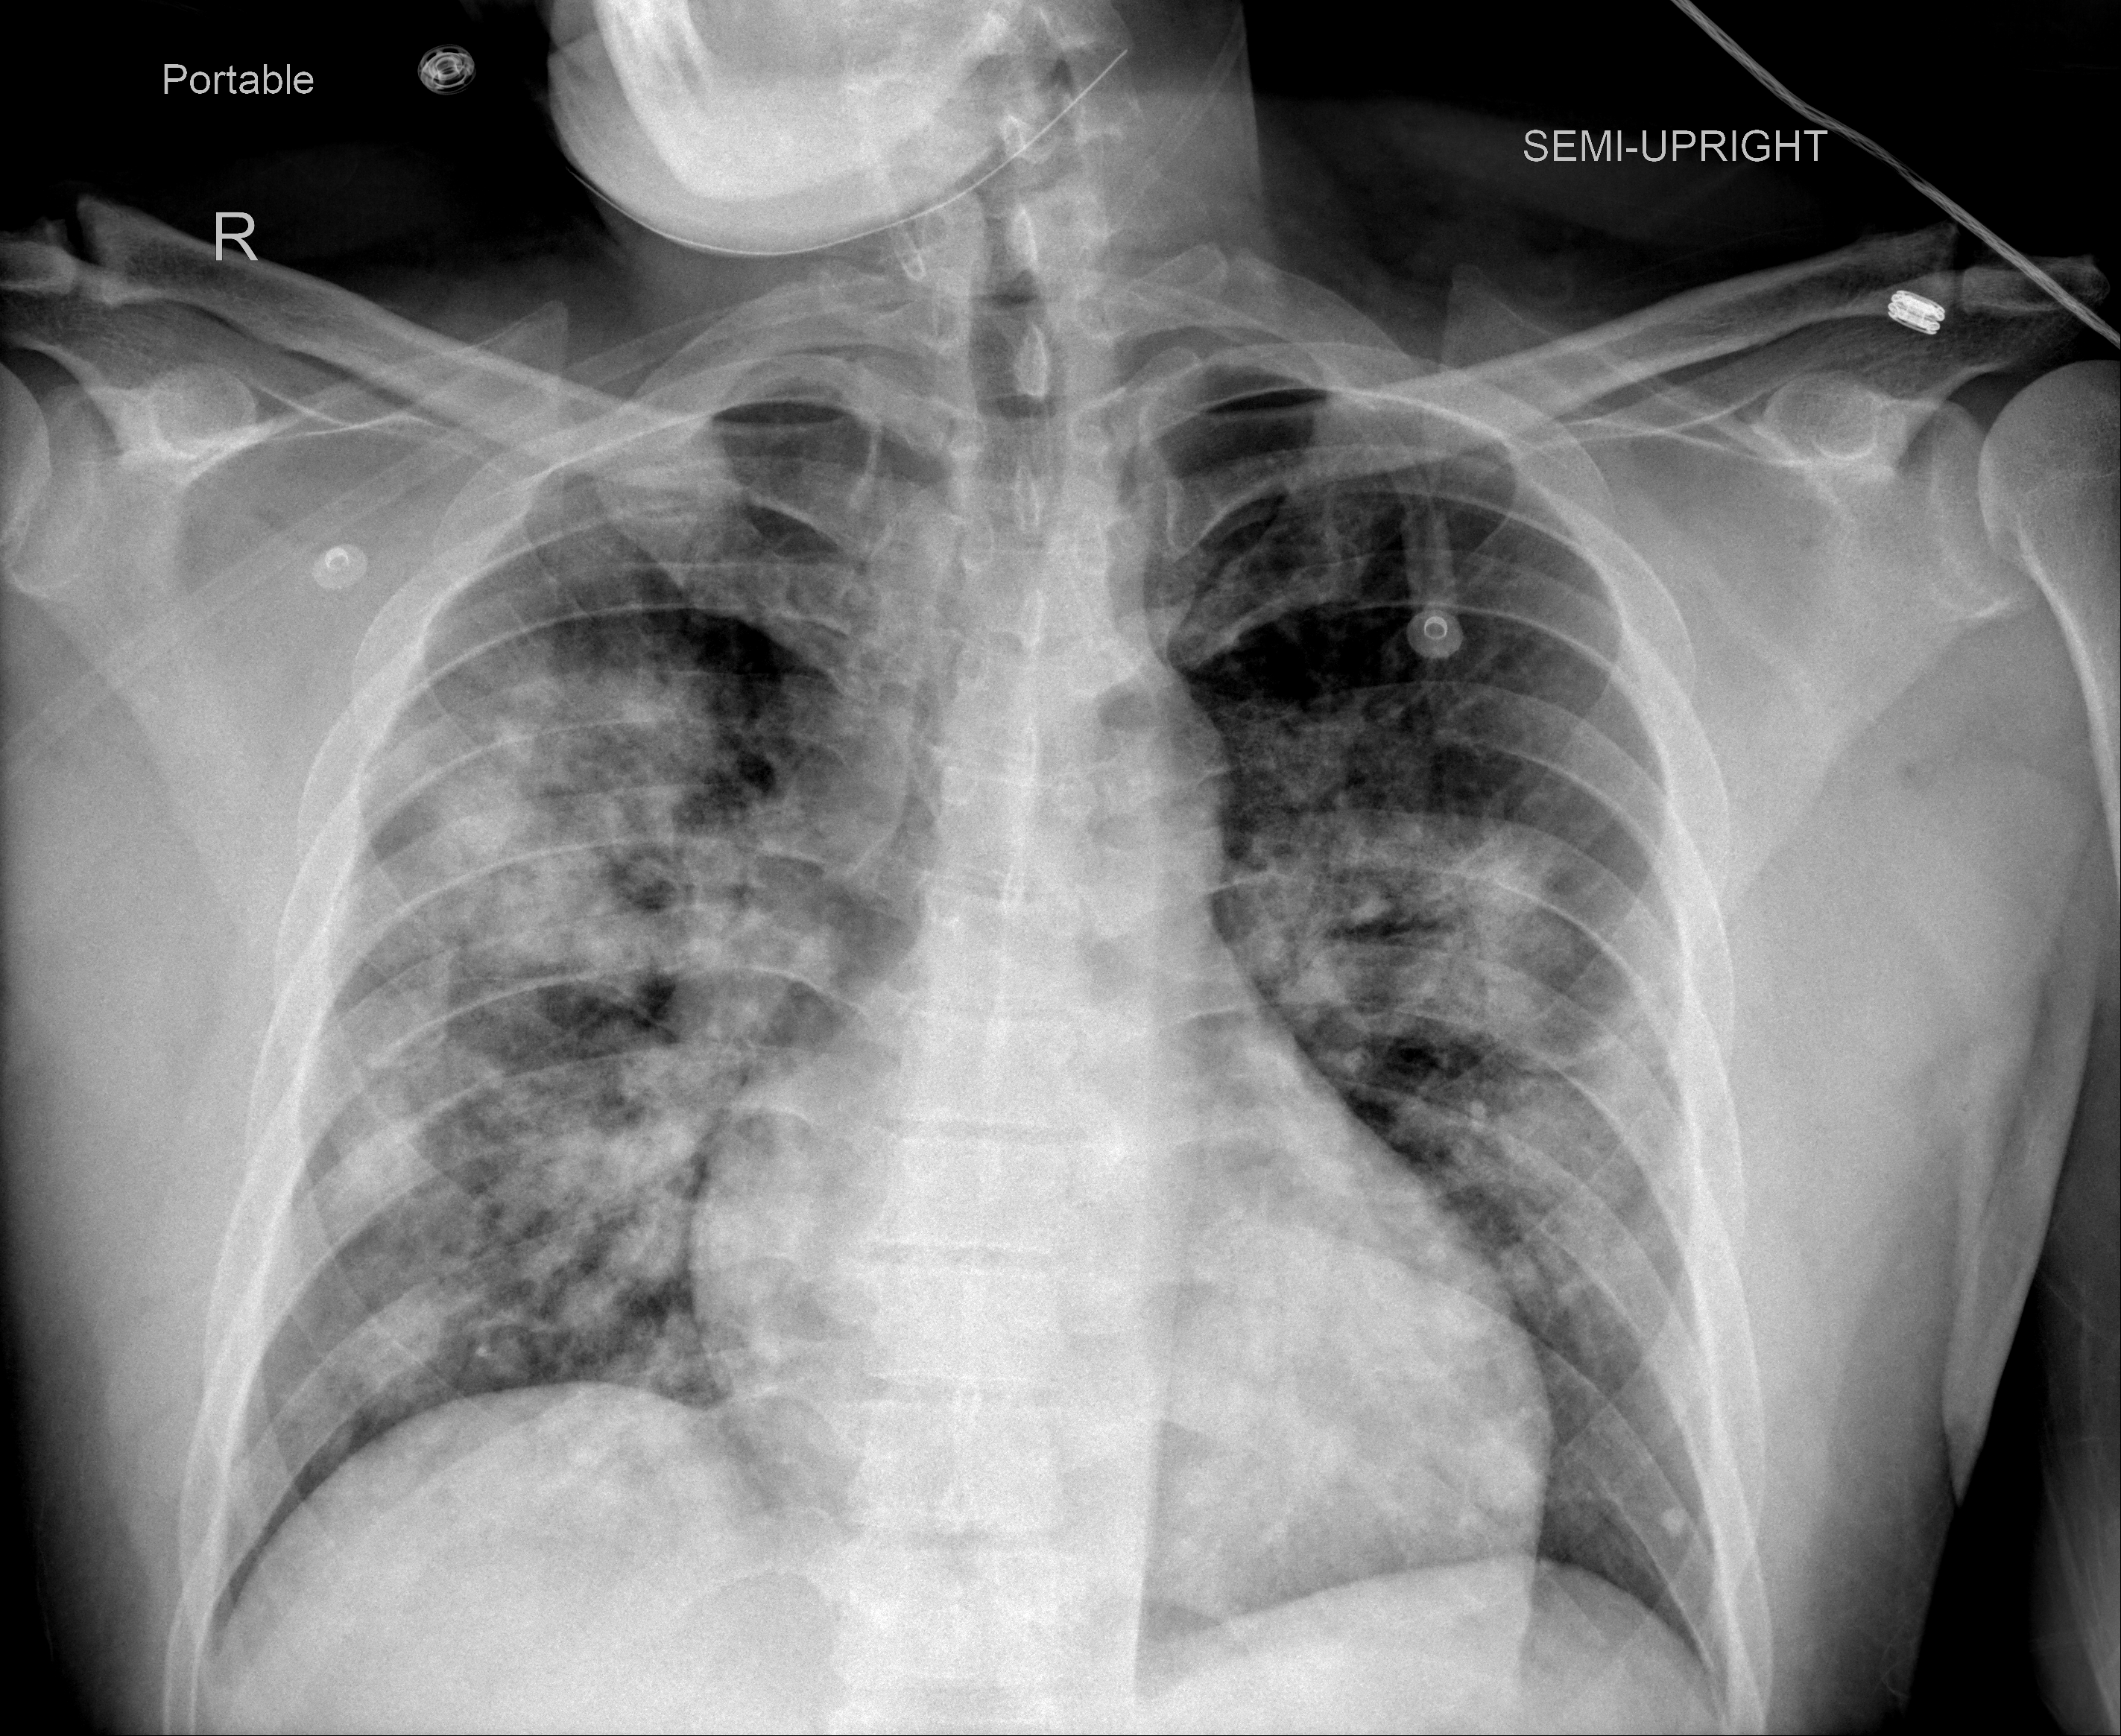
Portable chest radiograph, AP projection. Male patient, age 48 years; imaged 3 days after the COVID-19 diagnosis.
Radiologist's key findings for this exam: significant worsening of bilateral patchy airspace changes involving all lung zones with relative sparing of both lung apices.